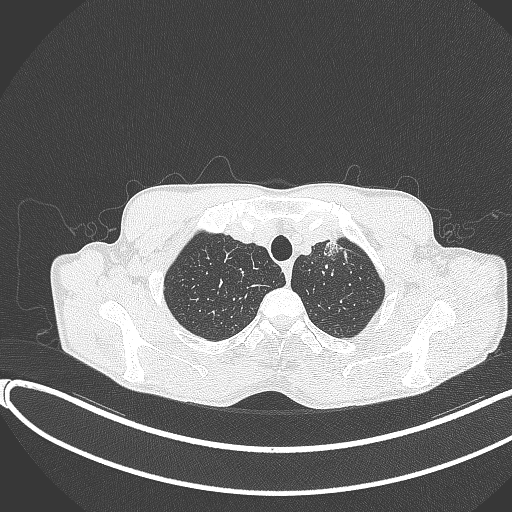
Chest CT, one axial slice. Position 339 of 374 along the scan axis. Lung window (W 1500 / L -600 HU). 512 × 512 image matrix, field of view 400 × 400 mm. Patient: male, 58 years. Case-level facts recorded for this patient, not image findings: clinical TNM (as recorded): T1c N1 M0.
Outlined on this slice (rectangle marked by the reading radiologist):
- lung tumour (recorded histology: adenocarcinoma): bounding box <322,234,348,256> (left, top, right, bottom; pixels)